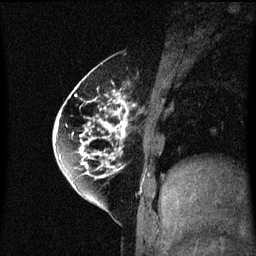
Breast MRI (dynamic contrast-enhanced), one sagittal slice; position 21 of 60 along the scan axis; dynamic contrast-enhanced series, image 2 of 3 at this slice position (ordered by acquisition); 1.5 T; TE 4.2 ms, TR 8.4 ms; 2 mm slice thickness; 256 × 256 image matrix. Patient: female, 60 years.
Annotated regions visible in this slice (semi-automatically segmented with operator editing):
- analysis volume of interest (the breast-tissue region the enhancement analysis was run in; not a lesion): bounding box [x1, y1, x2, y2] px = [64, 70, 133, 195]
- tumour enhancement mask (voxels above the 70 % enhancement threshold inside the analysis volume of interest): [64, 70, 129, 189]